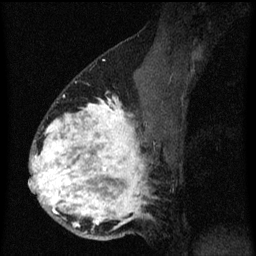
Breast MRI (dynamic contrast-enhanced), one sagittal slice; position 40 of 60 along the scan axis; dynamic contrast-enhanced series, image 2 of 3 at this slice position (ordered by acquisition); 1.5 T; TE 4.2 ms, TR 8.4 ms; 2 mm slice thickness; 256 × 256 image matrix, field of view 180 × 180 mm. Female patient, age 34 years. Case-level facts recorded for this patient, not image findings: setting: breast cancer imaged before/during neoadjuvant chemotherapy; receptor status: HR-positive, HER2-negative.
Structures marked on this image (semi-automatically segmented with operator editing):
- analysis volume of interest (the breast-tissue region the enhancement analysis was run in; not a lesion): bounding box [x1, y1, x2, y2] px = [30, 58, 165, 241]
- tumour enhancement mask (voxels above the 70 % enhancement threshold inside the analysis volume of interest): [30, 98, 149, 229]